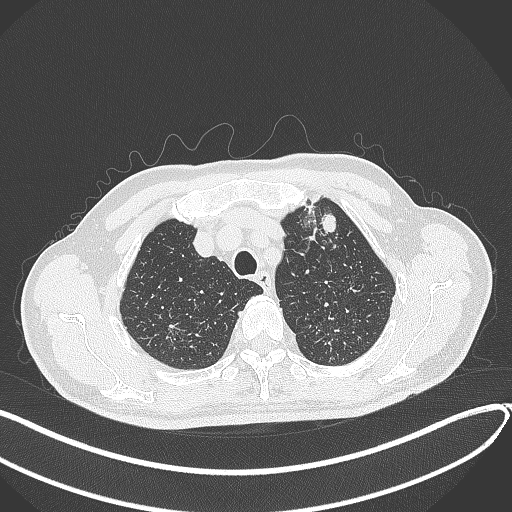
Chest CT, one axial slice. Position 353 of 459 along the scan axis. 120 kVp. Lung window (W 1500 / L -600 HU). 1 mm slice thickness. 512 × 512 image matrix, field of view 400 × 400 mm. Male patient, age 74 years. From the clinical record (not read from this slice): clinical TNM (as recorded): T2b N0 M1c.
Structures marked on this image (rectangle marked by the reading radiologist):
- lung tumour (recorded histology: adenocarcinoma): bounding box (x1, y1, x2, y2) in pixels: (320, 208, 341, 236)